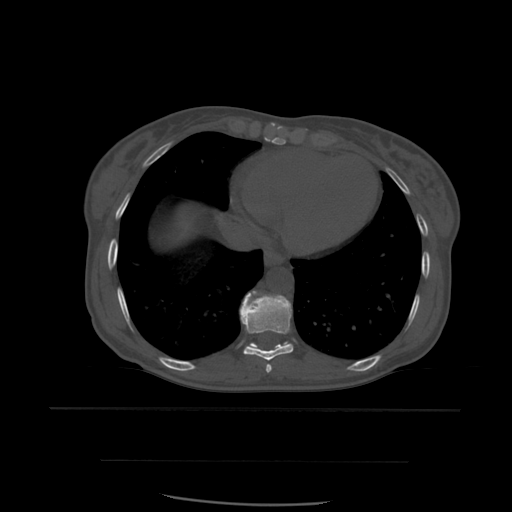
CT including the spine, one axial slice; slice 333 of 574 in the series (ordered by position); bone window (W 1800 / L 400 HU); 512 × 512 image matrix, field of view 392 × 392 mm. Patient age 48 years. From the clinical record (not read from this slice): primary cancer: lung; vertebrae with lytic lesions (as recorded): T11.
Structures marked on this image (semi-automatically segmented with operator editing):
- T10 vertebra: box from (x=251, y=343) to (x=285, y=346) px
- T8 vertebra: (x=266, y=364)–(x=272, y=373)
- T9 vertebra: (x=240, y=291)–(x=294, y=361)